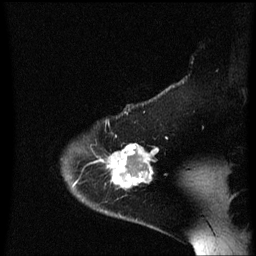
Breast MRI (dynamic contrast-enhanced), one sagittal slice. Slice 50 of 60 in the series (ordered by position). Dynamic contrast-enhanced series, image 2 of 3 at this slice position (ordered by acquisition). 1.5 T. TE 4.2 ms, TR 8.4 ms. 256 × 256 image matrix, field of view 200 × 200 mm. Female patient, age 54 years. From the clinical record (not read from this slice): setting: breast cancer imaged before/during neoadjuvant chemotherapy; receptor status: HR-positive, HER2-negative.
Outlined on this slice (semi-automatic segmentation, software-assisted and operator-edited):
- analysis volume of interest (the breast-tissue region the enhancement analysis was run in; not a lesion): bounding box (x1, y1, x2, y2) in pixels: (102, 132, 161, 197)
- tumour enhancement mask (voxels above the 70 % enhancement threshold inside the analysis volume of interest): (107, 144, 160, 189)